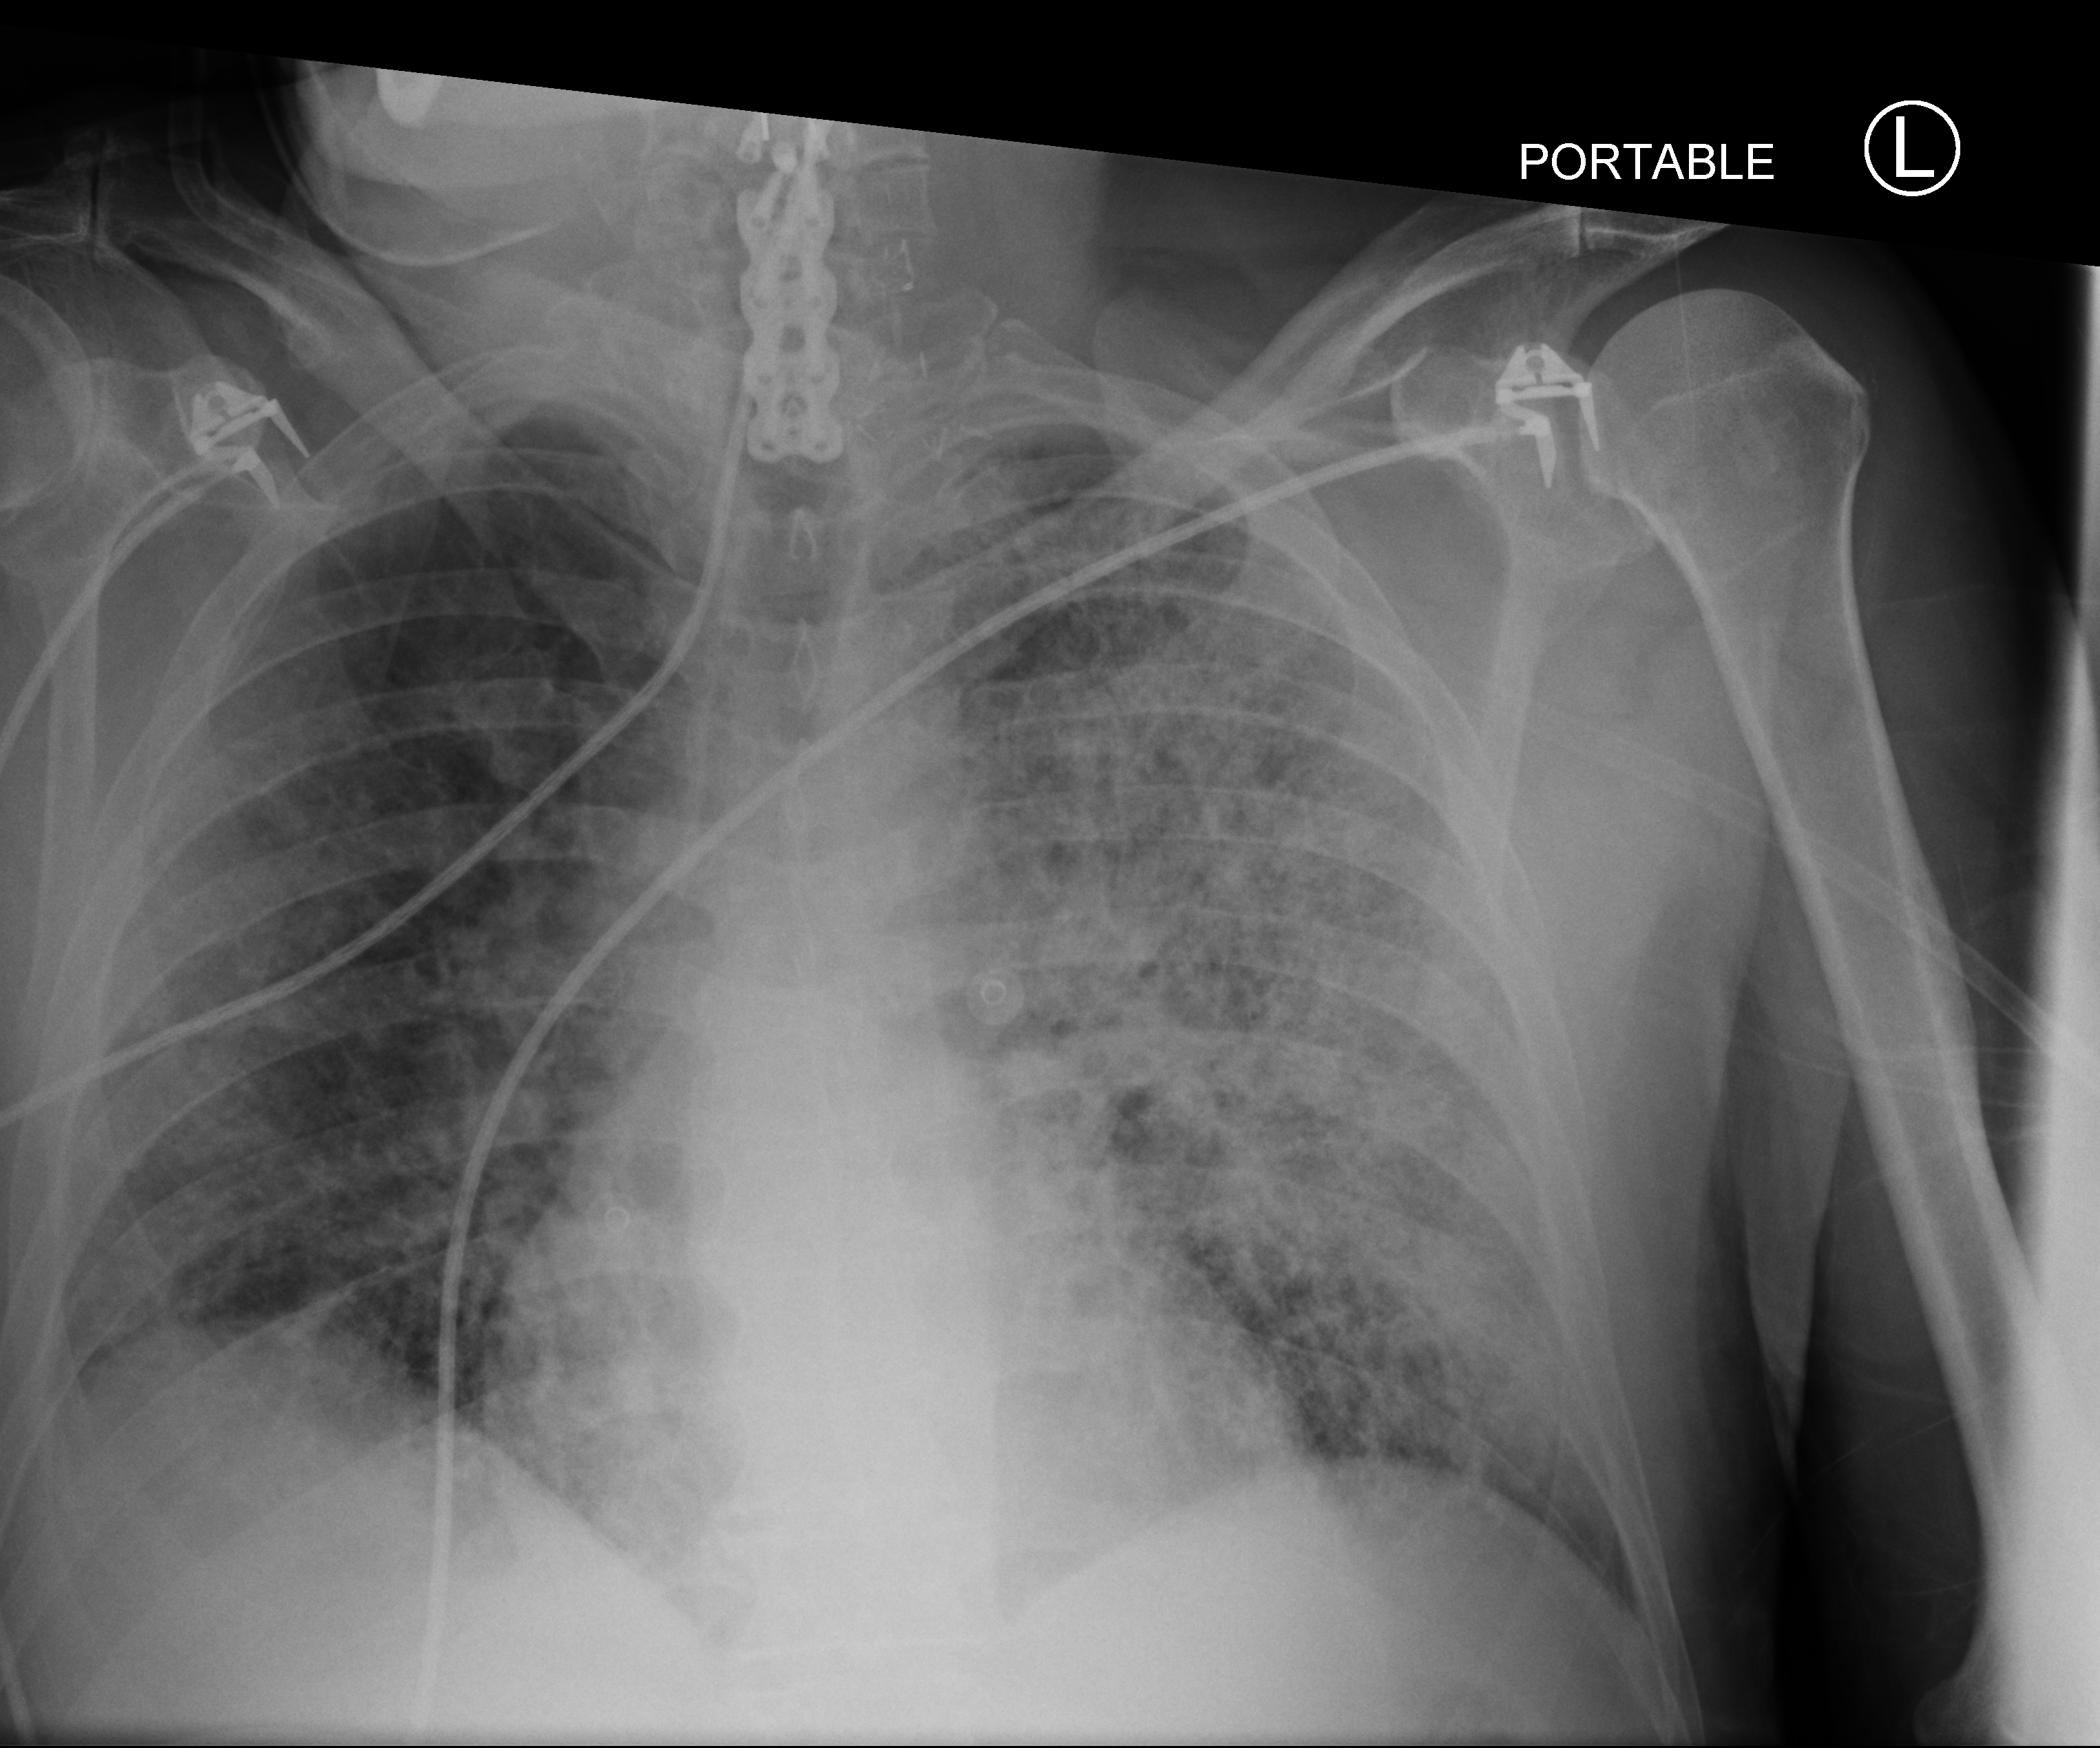
Portable chest radiograph, anteroposterior (AP) projection. Male patient hospitalised with COVID-19, age 60–74 years.
Hospital-stay facts (about this admission, not read from this image; timing relative to this image not recorded): admitted to intensive care during this hospital stay: yes; mechanically ventilated during this hospital stay: yes.